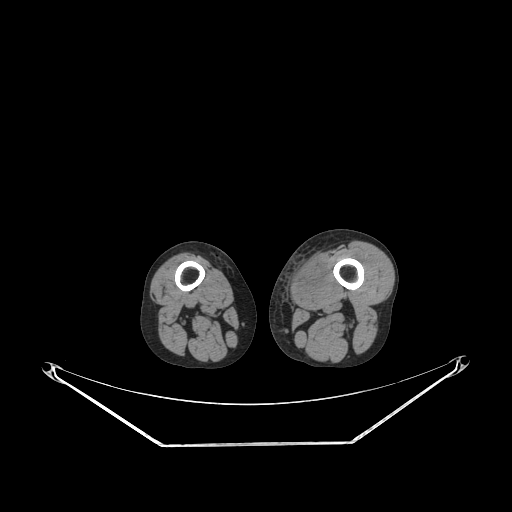
CT of an extremity soft-tissue mass (from a PET/CT study), one axial slice; reconstruction kernel STANDARD; soft-tissue window (W 400 / L 40 HU); 3.75 mm slice thickness; 512 × 512 image matrix, field of view 500 × 500 mm. Male patient. From the clinical record (not read from this slice): histological type: pleiomorphic leiomyosarcoma; grade: high; site of the primary tumour: left thigh.
Annotated regions visible in this slice (expert contour drawn on MRI and transferred to this co-registered scan by the dataset authors):
- gross tumour volume including surrounding oedema: bounding box [x1, y1, x2, y2] px = [290, 253, 328, 305]